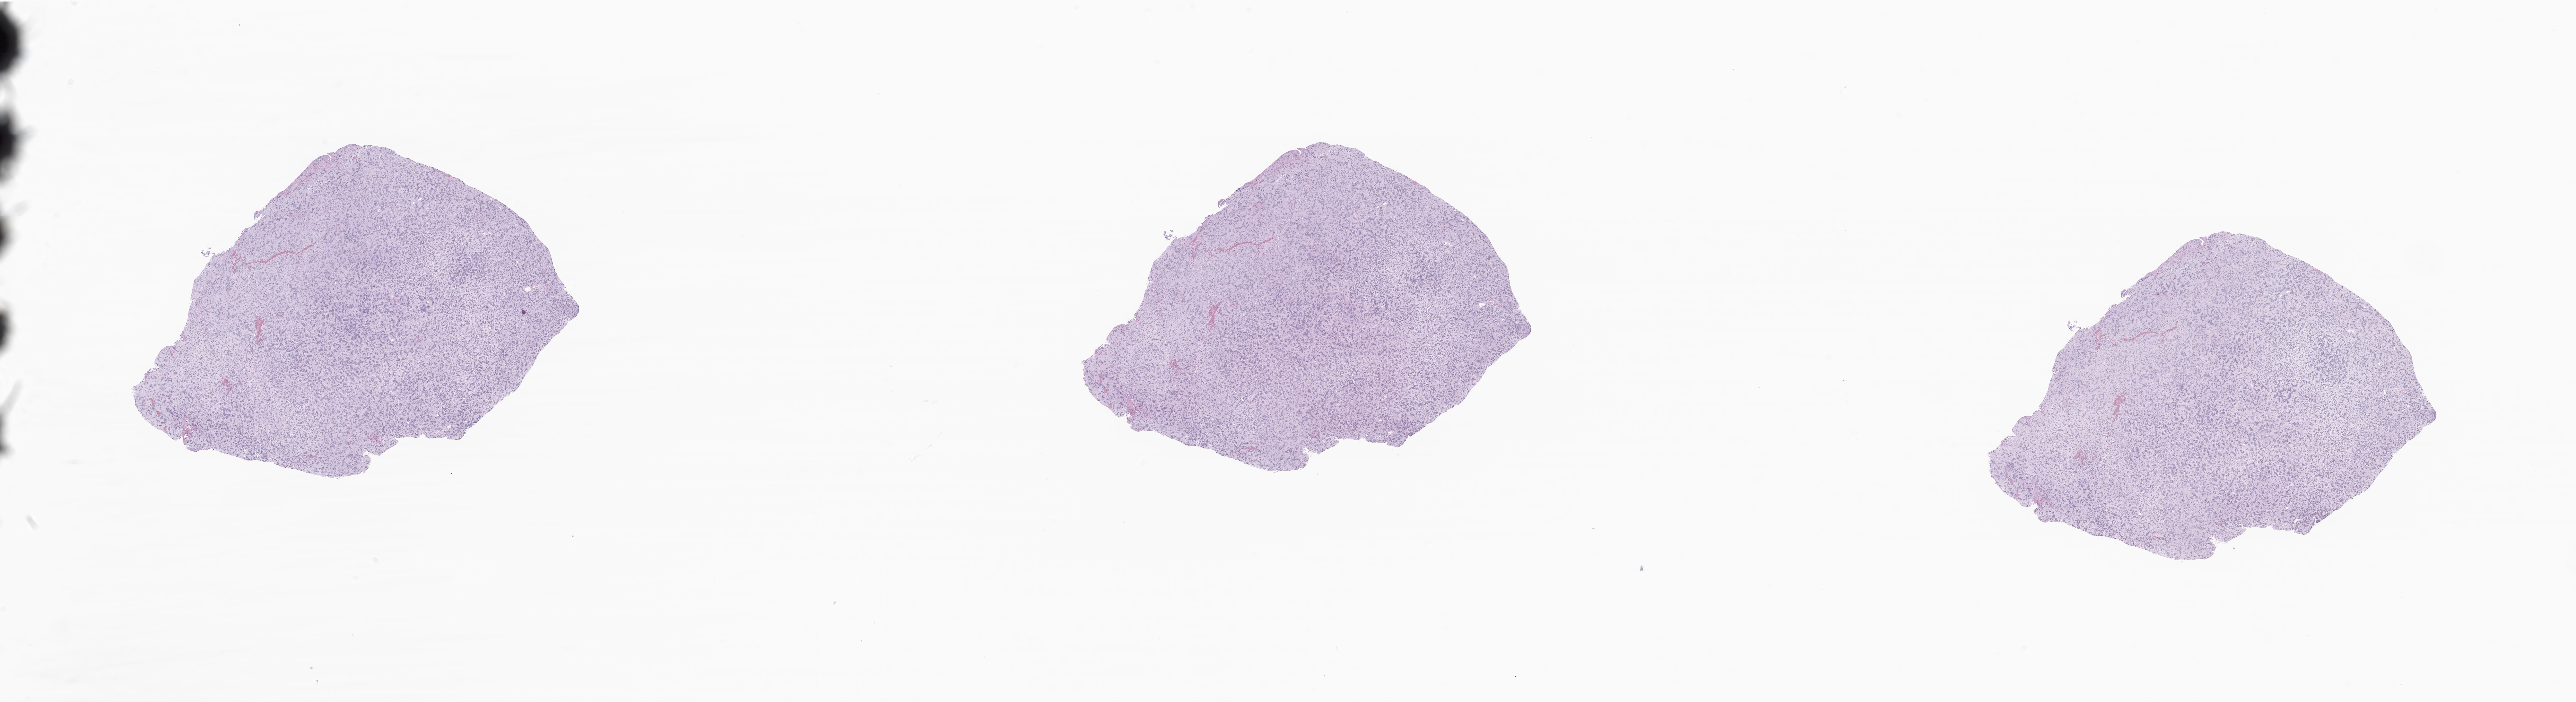
Digitized H&E-stained section of tumor tissue from the brain, low-resolution overview of the scanned area, about 33.8 x 9.2 mm, FFPE section. Patient male; age 123 months (10 years 3 months).
- diagnosis: Ependymoma, NOS